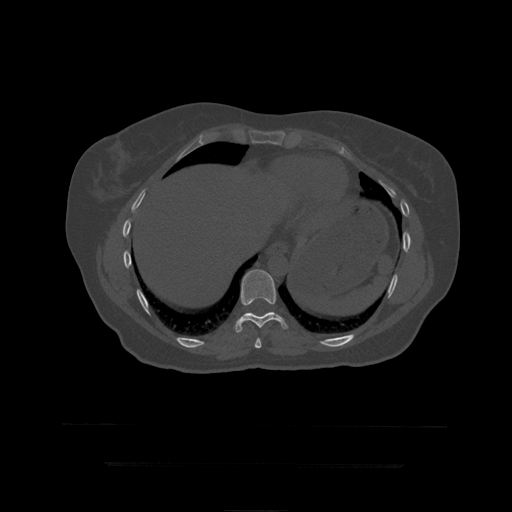
CT including the spine, one axial slice. Slice 241 of 399 in the series (ordered by position). 120 kVp. Bone window (W 1800 / L 400 HU). 1.25 mm slice thickness. 512 × 512 image matrix, field of view 450 × 450 mm. Patient age 41 years. From the clinical record (not read from this slice): primary cancer: breast.
Outlined on this slice (semi-automatic segmentation, software-assisted and operator-edited):
- T10 vertebra: bounding box <235,270,289,333> (left, top, right, bottom; pixels)
- T9 vertebra: <255,338,262,350>